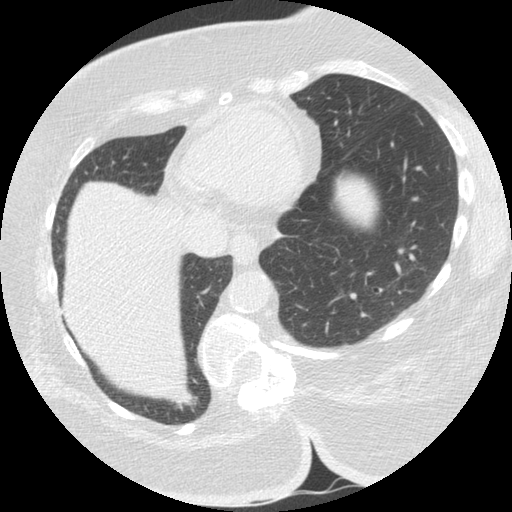
Low-dose screening chest CT, one axial slice; position 46 of 151 along the scan axis; 140 kVp; lung window (W 1500 / L -600 HU); 2.5 mm slice thickness; 512 × 512 image matrix.
Annotated regions visible in this slice (manually delineated by an expert):
- lesion 1 (tumor, lower lobe of right lung): box from (x=177, y=390) to (x=198, y=412) px